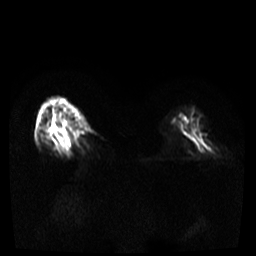
Breast MRI, one axial slice; position 10 of 36 along the scan axis; diffusion-weighted series; image 2 of 4 stored at this slice position (different b-values; order by instance number); 3 T; 256 × 256 image matrix. Female patient.
Structures marked on this image (outlined manually by an expert reader):
- tumour on diffusion-weighted imaging: bounding box (x1, y1, x2, y2) in pixels: (51, 127, 71, 155)